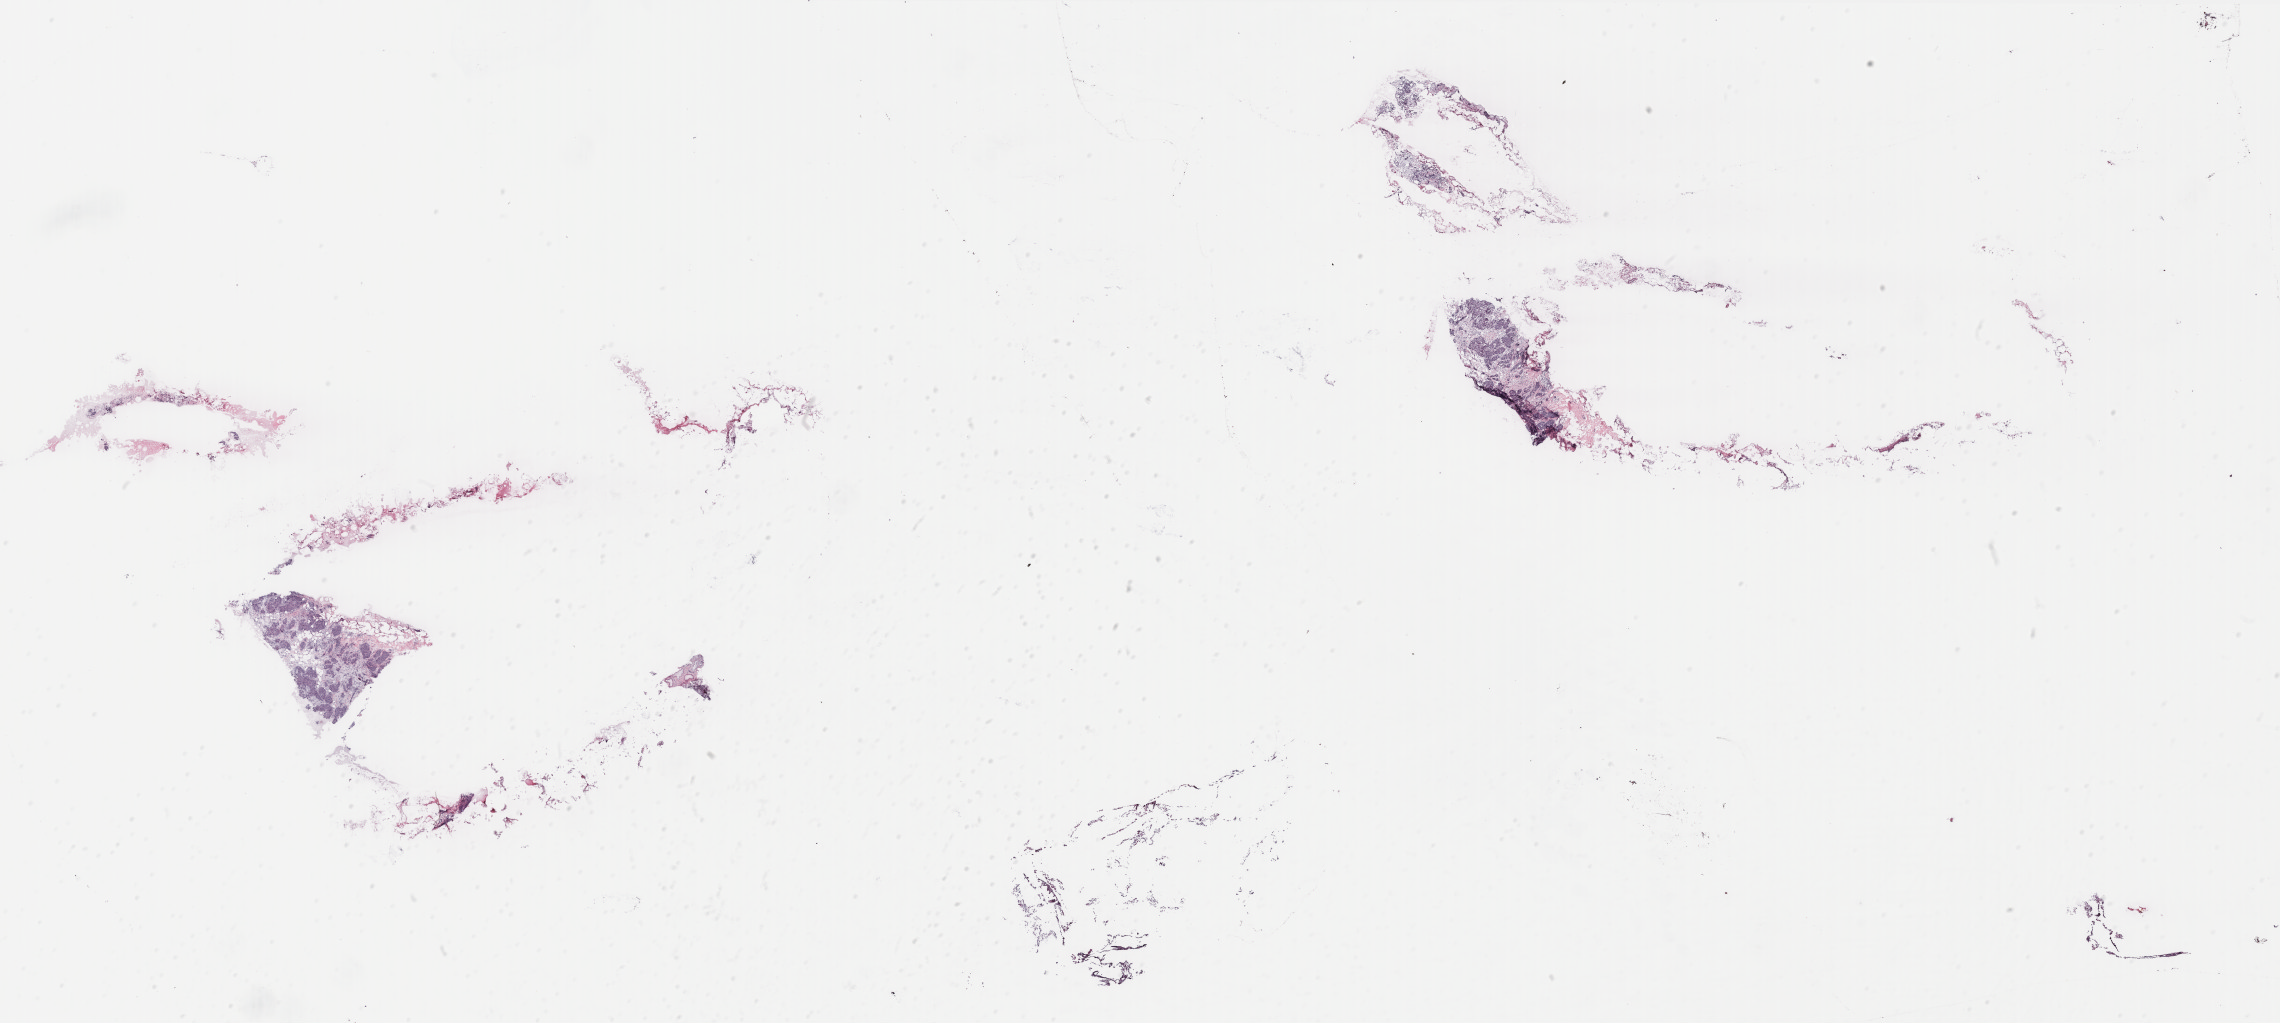
Whole-slide histology image, Hematoxylin and eosin (H&E) stained, low-resolution overview of the scanned area, about 36.5 x 16.4 mm (from a 40x scan), breast, tissue type not recorded.
Patient diagnosis (cohort enrolment): breast cancer (breast).